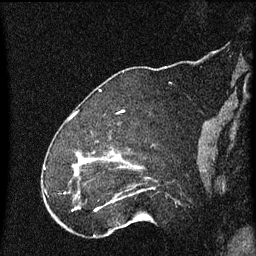
Breast MRI (dynamic contrast-enhanced), one sagittal slice. Position 18 of 60 along the scan axis. Dynamic contrast-enhanced series, image 2 of 4 at this slice position (ordered by acquisition). 1.5 T. TE 4.2 ms, TR 8 ms. 2 mm slice thickness. 256 × 256 image matrix. Patient: female, 52 years.
Annotated regions visible in this slice (semi-automatically segmented with operator editing):
- analysis volume of interest (the breast-tissue region the enhancement analysis was run in; not a lesion): bounding box (x1, y1, x2, y2) in pixels: (73, 148, 164, 219)
- tumour enhancement mask (voxels above the 70 % enhancement threshold inside the analysis volume of interest): (74, 160, 118, 211)